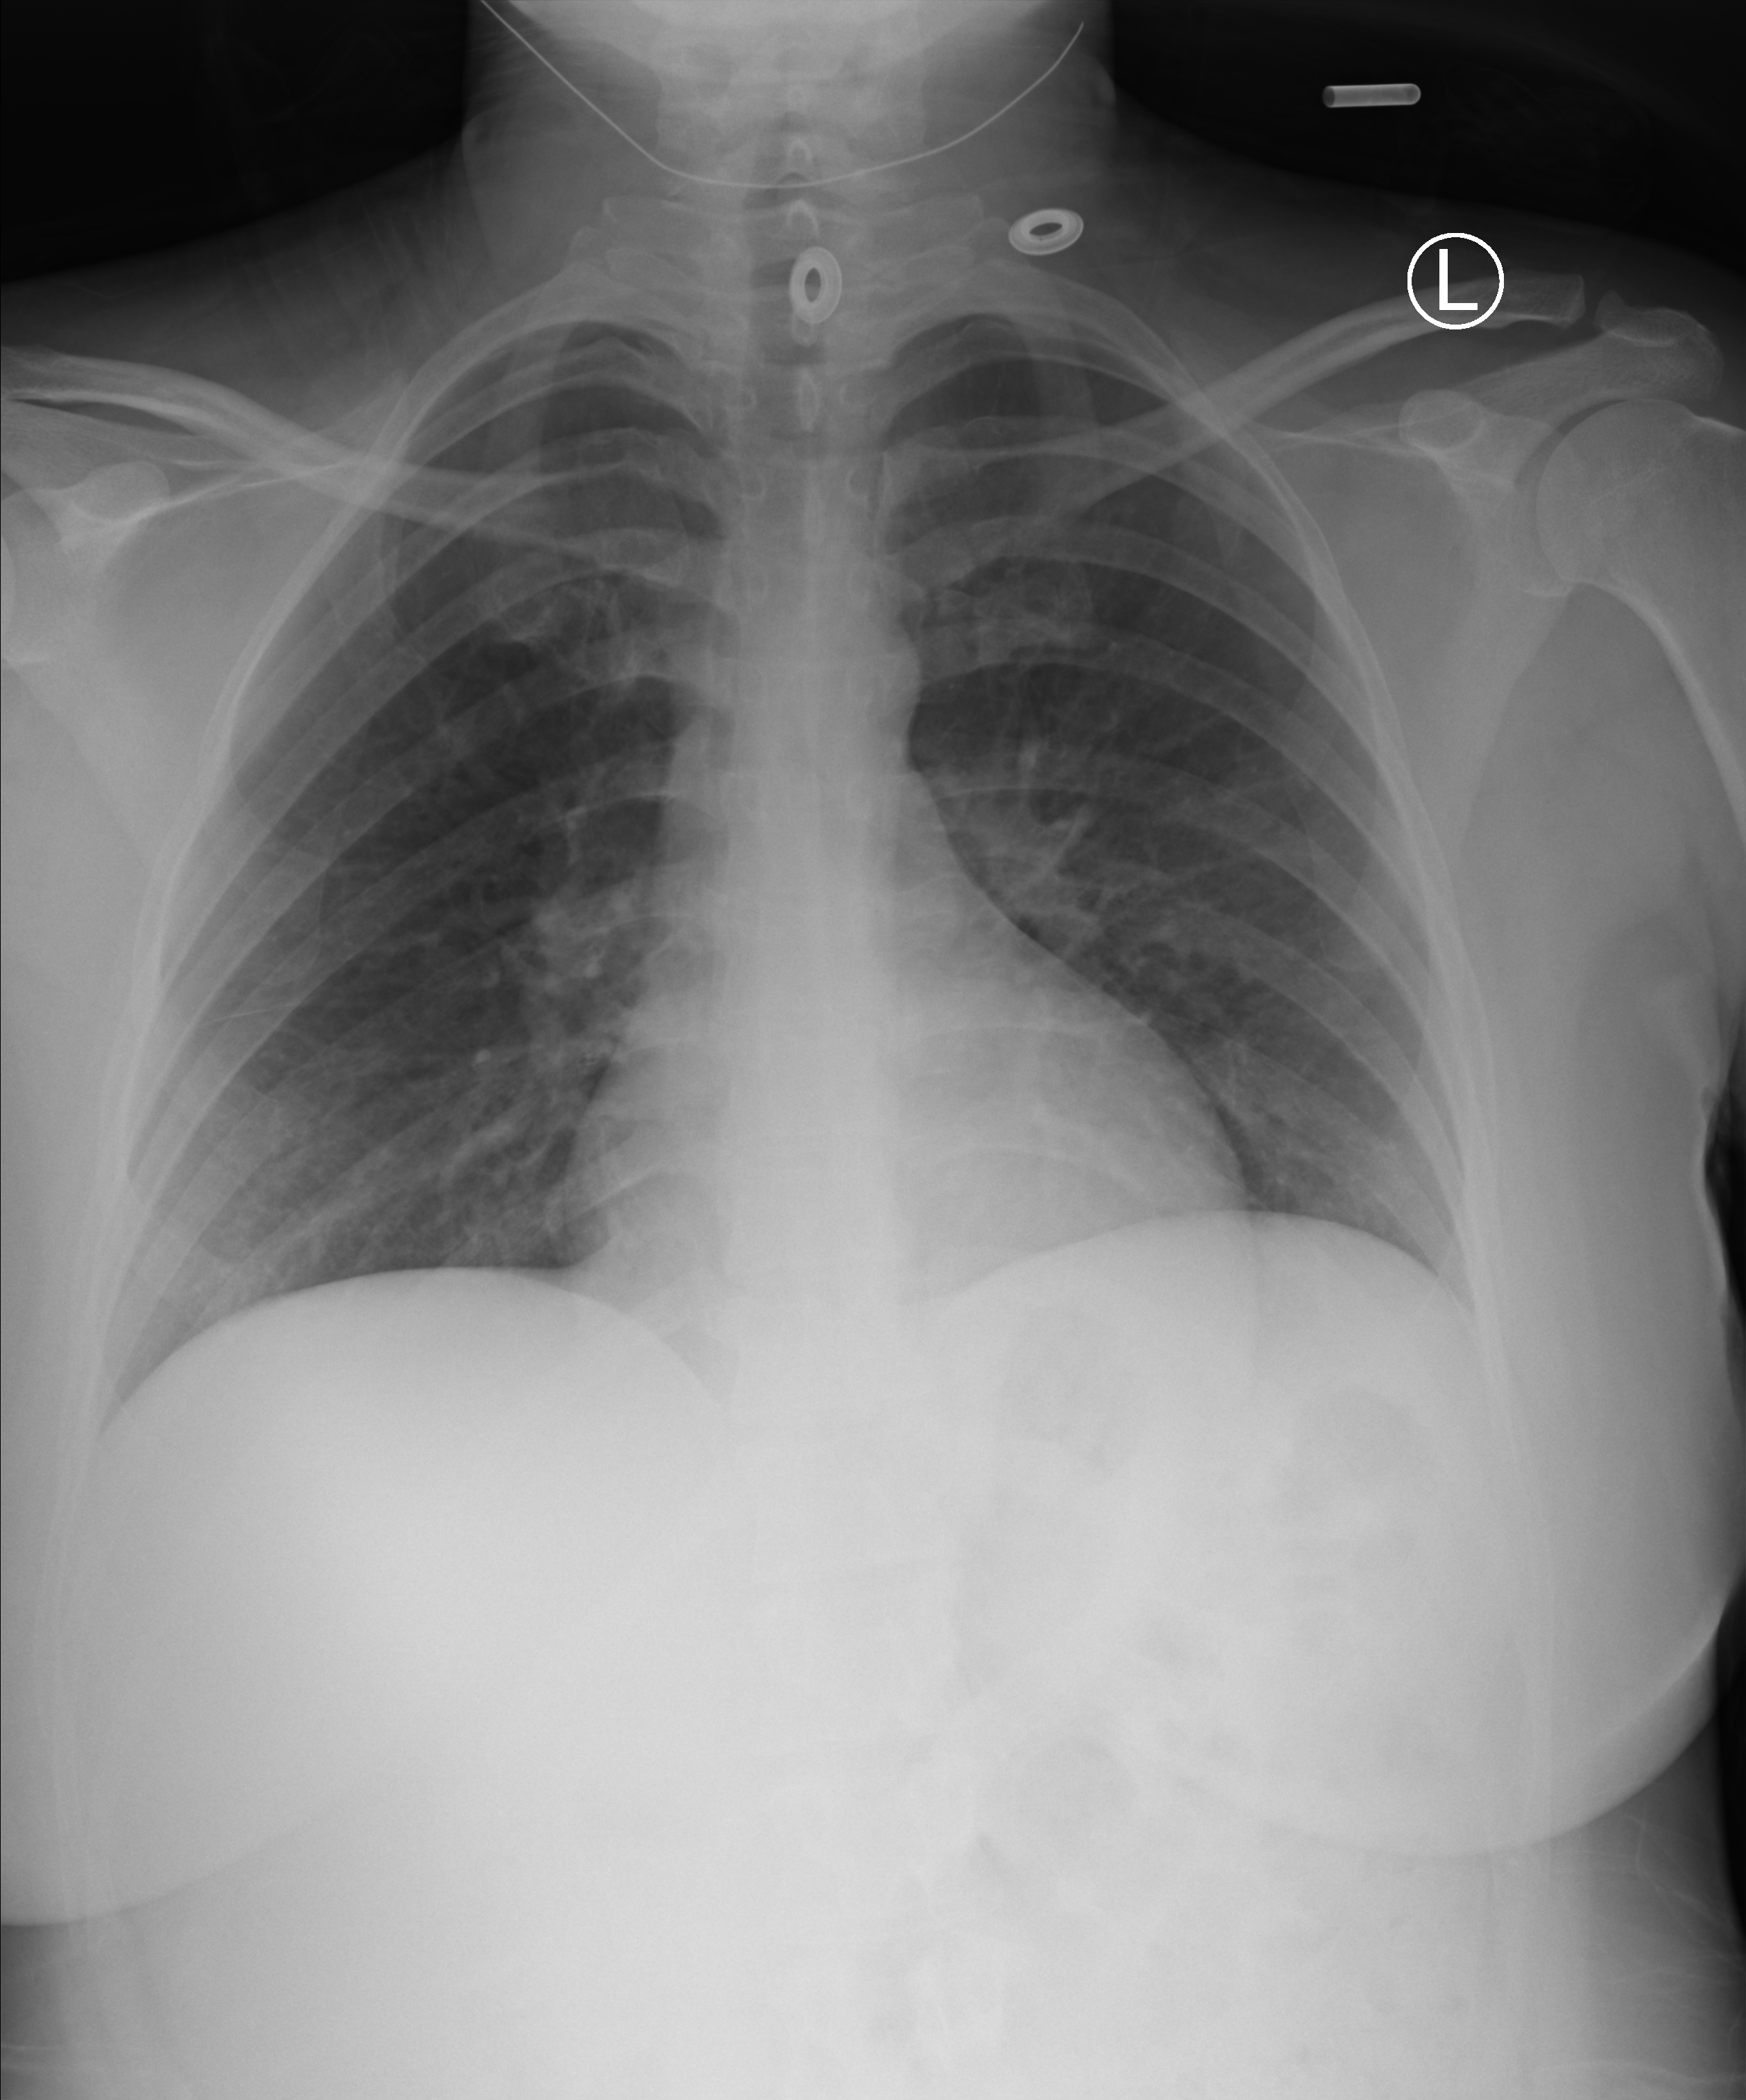
Bedside chest radiograph (computed radiography); anteroposterior (AP) projection. Female patient hospitalised with COVID-19, age 18–59 years.
From the hospital-stay record, not from the radiograph (when in the stay this image was taken is not recorded):
- mechanically ventilated during this hospital stay: no
- other chronic lung disease (admission record): no